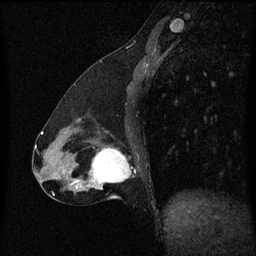
Breast MRI (dynamic contrast-enhanced), one sagittal slice; slice 24 of 60 in the series (ordered by position); dynamic contrast-enhanced series, image 2 of 3 at this slice position (ordered by acquisition); 1.5 T; TE 4.2 ms, TR 8.4 ms; 2 mm slice thickness; 256 × 256 image matrix, field of view 200 × 200 mm. Female patient, age 47 years.
Structures marked on this image (semi-automatic segmentation, software-assisted and operator-edited):
- analysis volume of interest (the breast-tissue region the enhancement analysis was run in; not a lesion): bounding box [x1, y1, x2, y2] px = [81, 144, 131, 197]
- tumour enhancement mask (voxels above the 70 % enhancement threshold inside the analysis volume of interest): [91, 148, 131, 185]